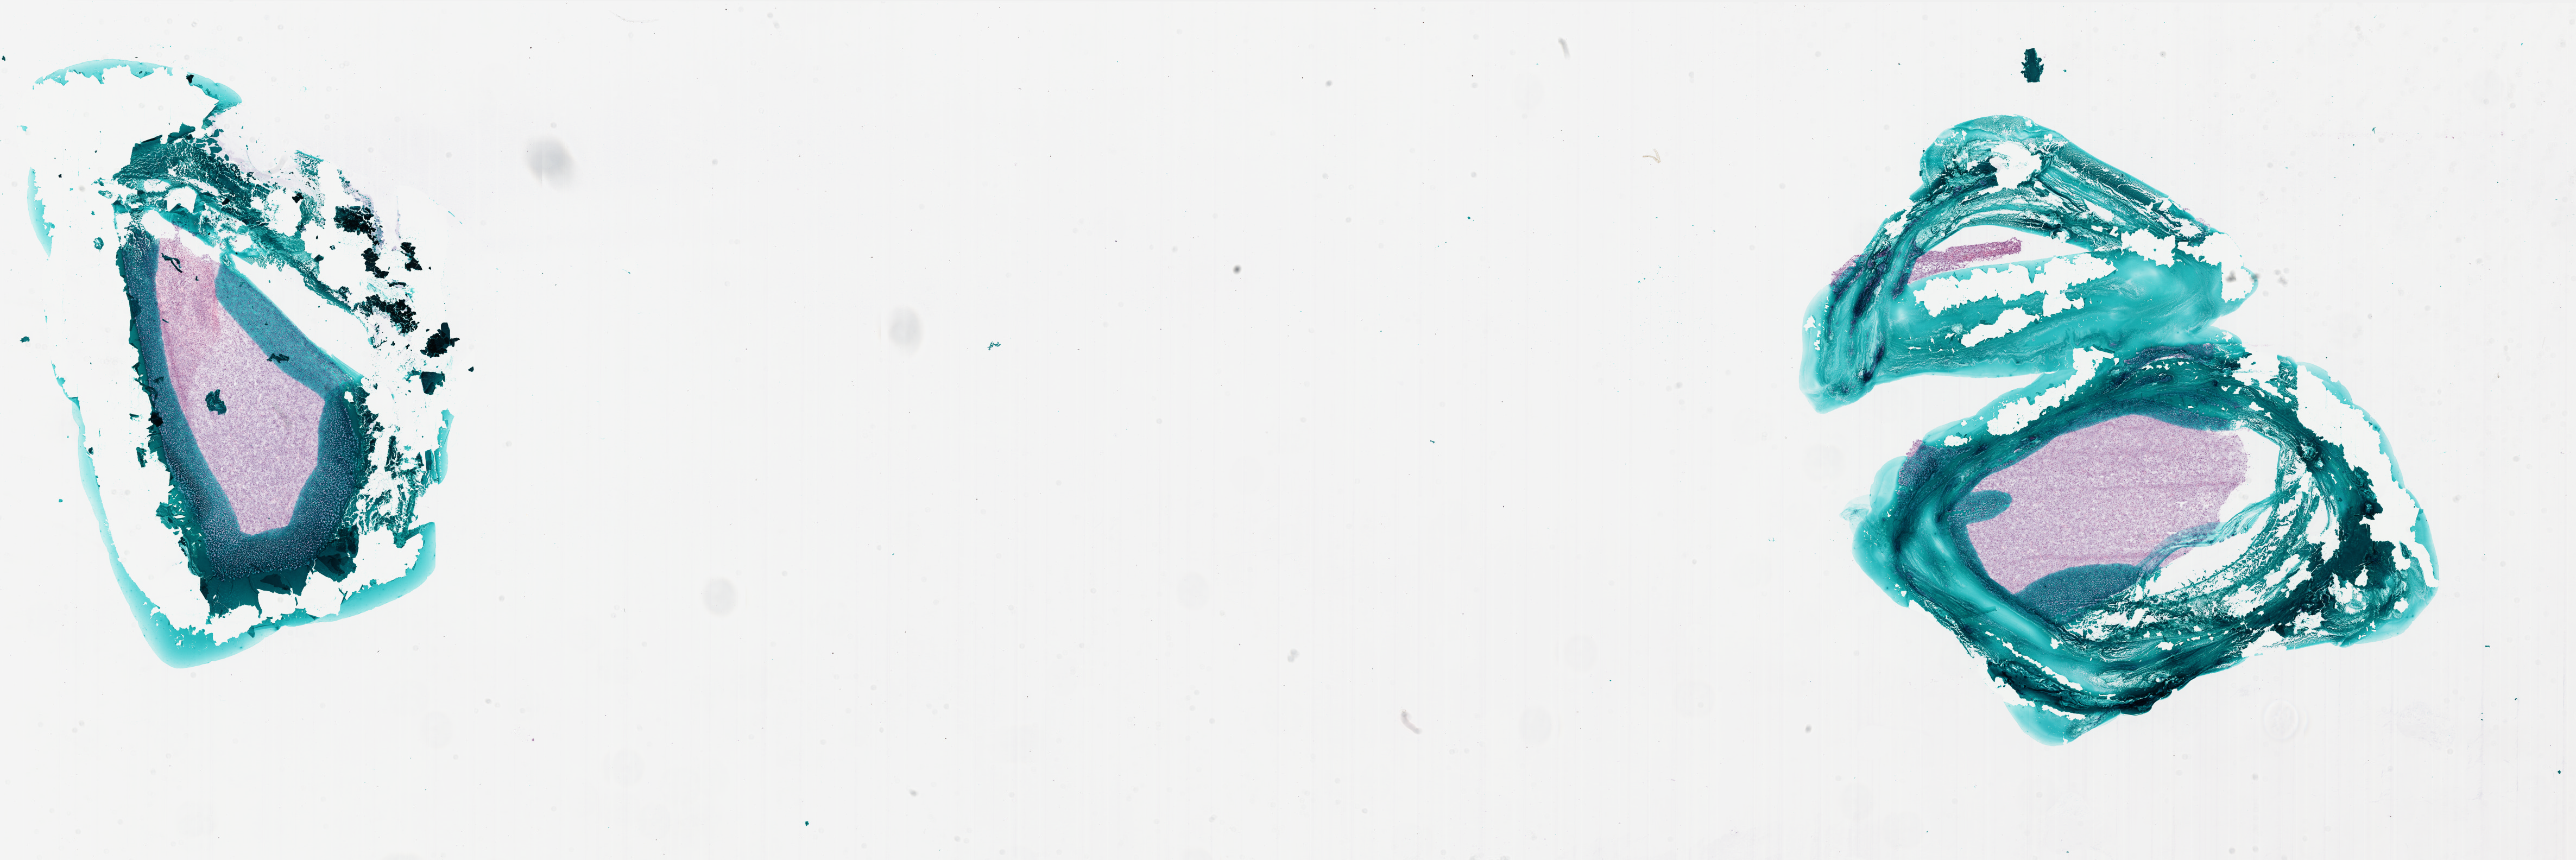
Whole-slide histology image, H&E, whole scanned area (about 38.0 x 12.7 mm, from a 20x scan) shown as a low-resolution overview, frozen section from the bottom of the tissue portion, brain, primary tumour sample. Patient: female, age at initial diagnosis 18 years. Pathologist review of this section (percent, as recorded): tumour cells 100%, tumour nuclei 100%, normal cells 0%, stromal cells 0%, necrosis 0%.
Diagnosis: Glioblastoma.